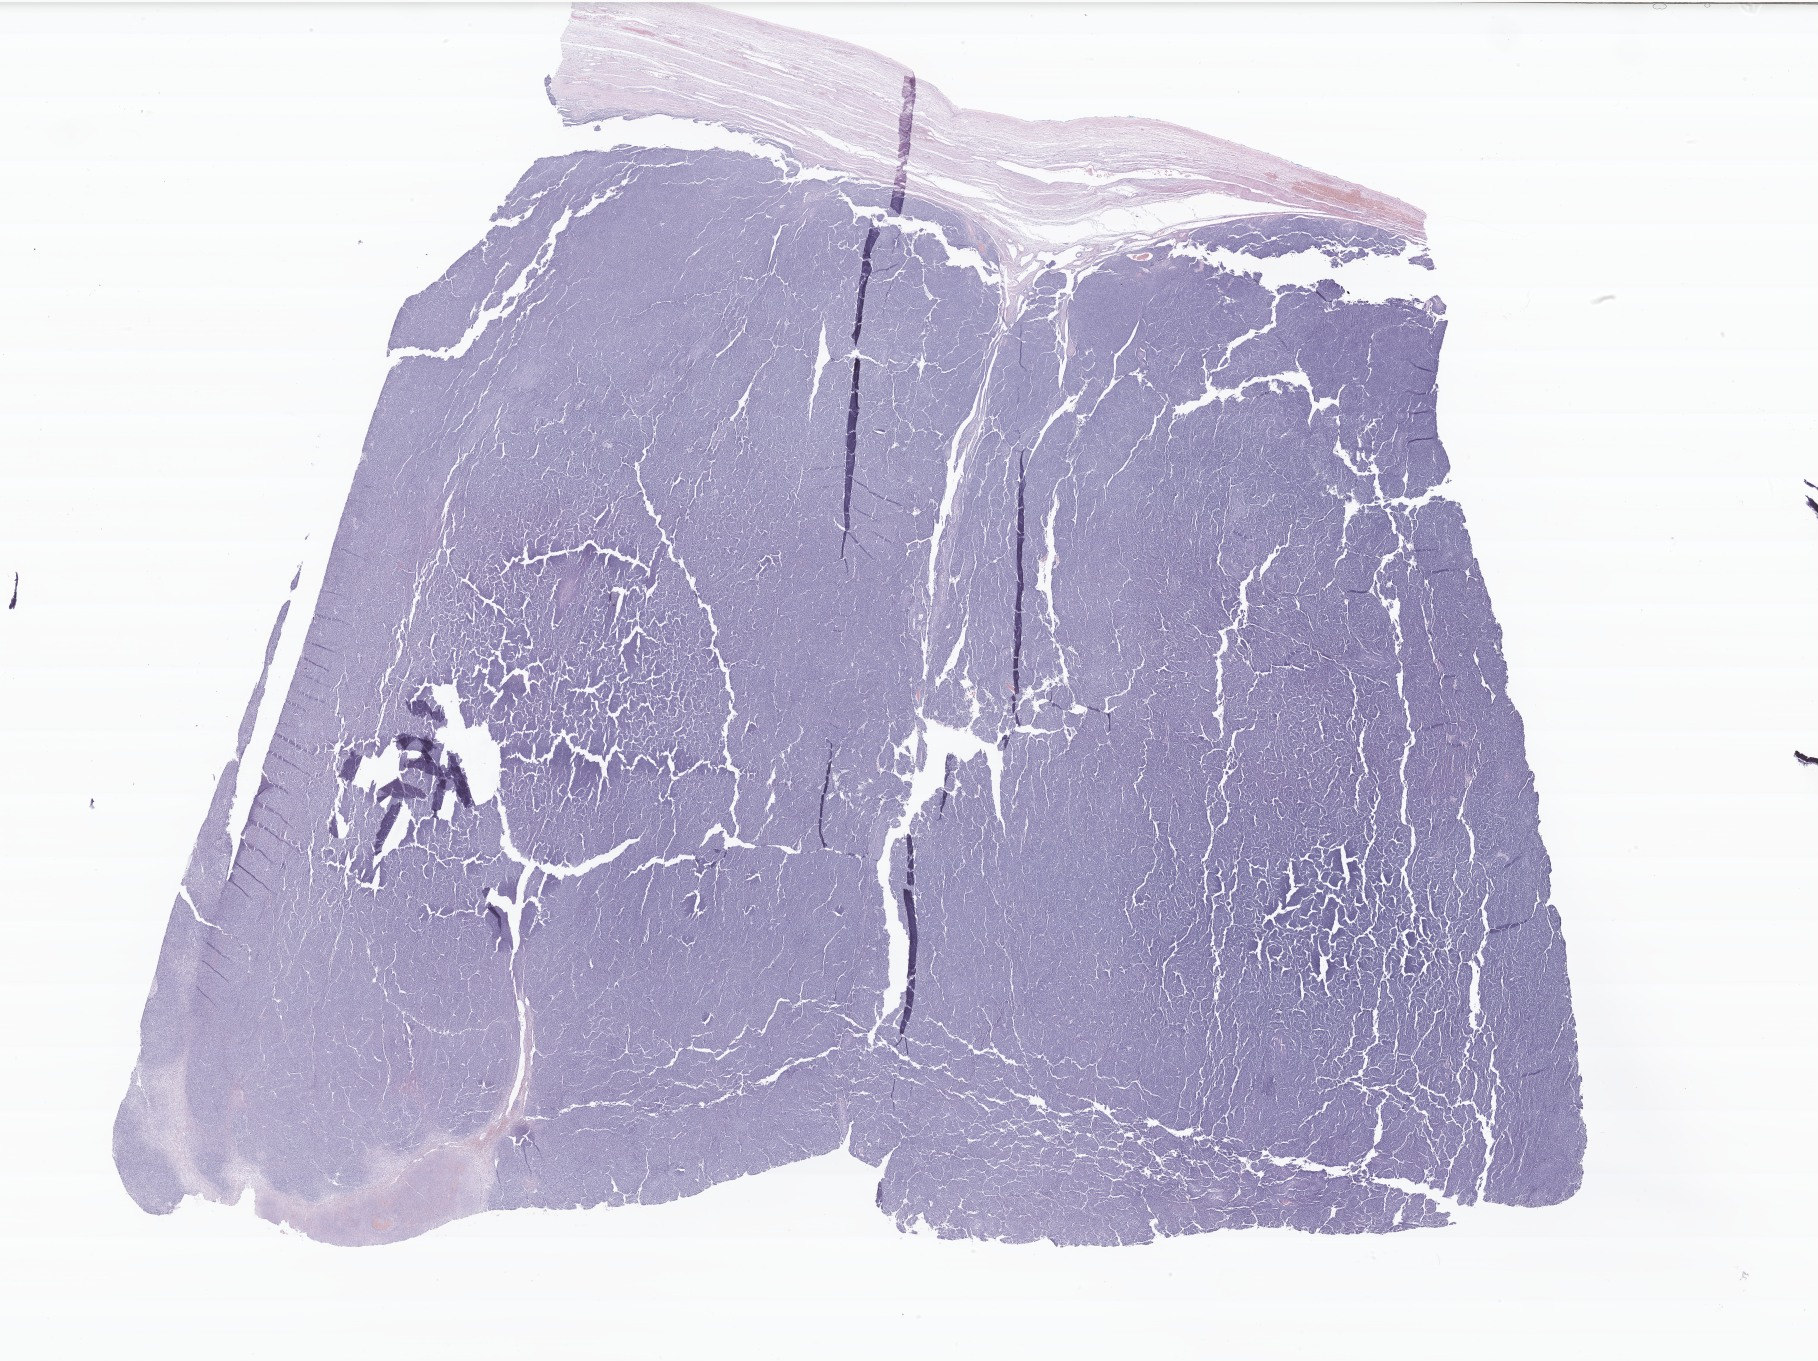
Whole-slide image, hematoxylin and eosin (H&E) stain of tumor tissue from the ovary — a low-resolution overview of the entire scanned area, about 30.6 x 22.9 mm. FFPE section. Patient female; age 173 months (14 years 5 months).
* recorded diagnosis: Sertoli-Leydig cell tumor, poorly differentiated